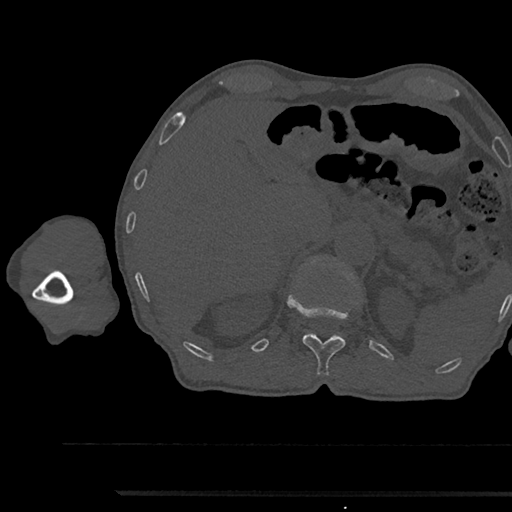
CT including the spine, one axial slice. Position 695 of 797 along the scan axis. Reconstruction kernel Br40s/3. 120 kVp. Bone window (W 1800 / L 400 HU). 512 × 512 image matrix, field of view 367 × 367 mm. Patient: male, 79 years. From the clinical record (not read from this slice): primary cancer: prostate.
Structures marked on this image (semi-automatically segmented with operator editing):
- T12 vertebra: box from (x=289, y=299) to (x=346, y=375) px